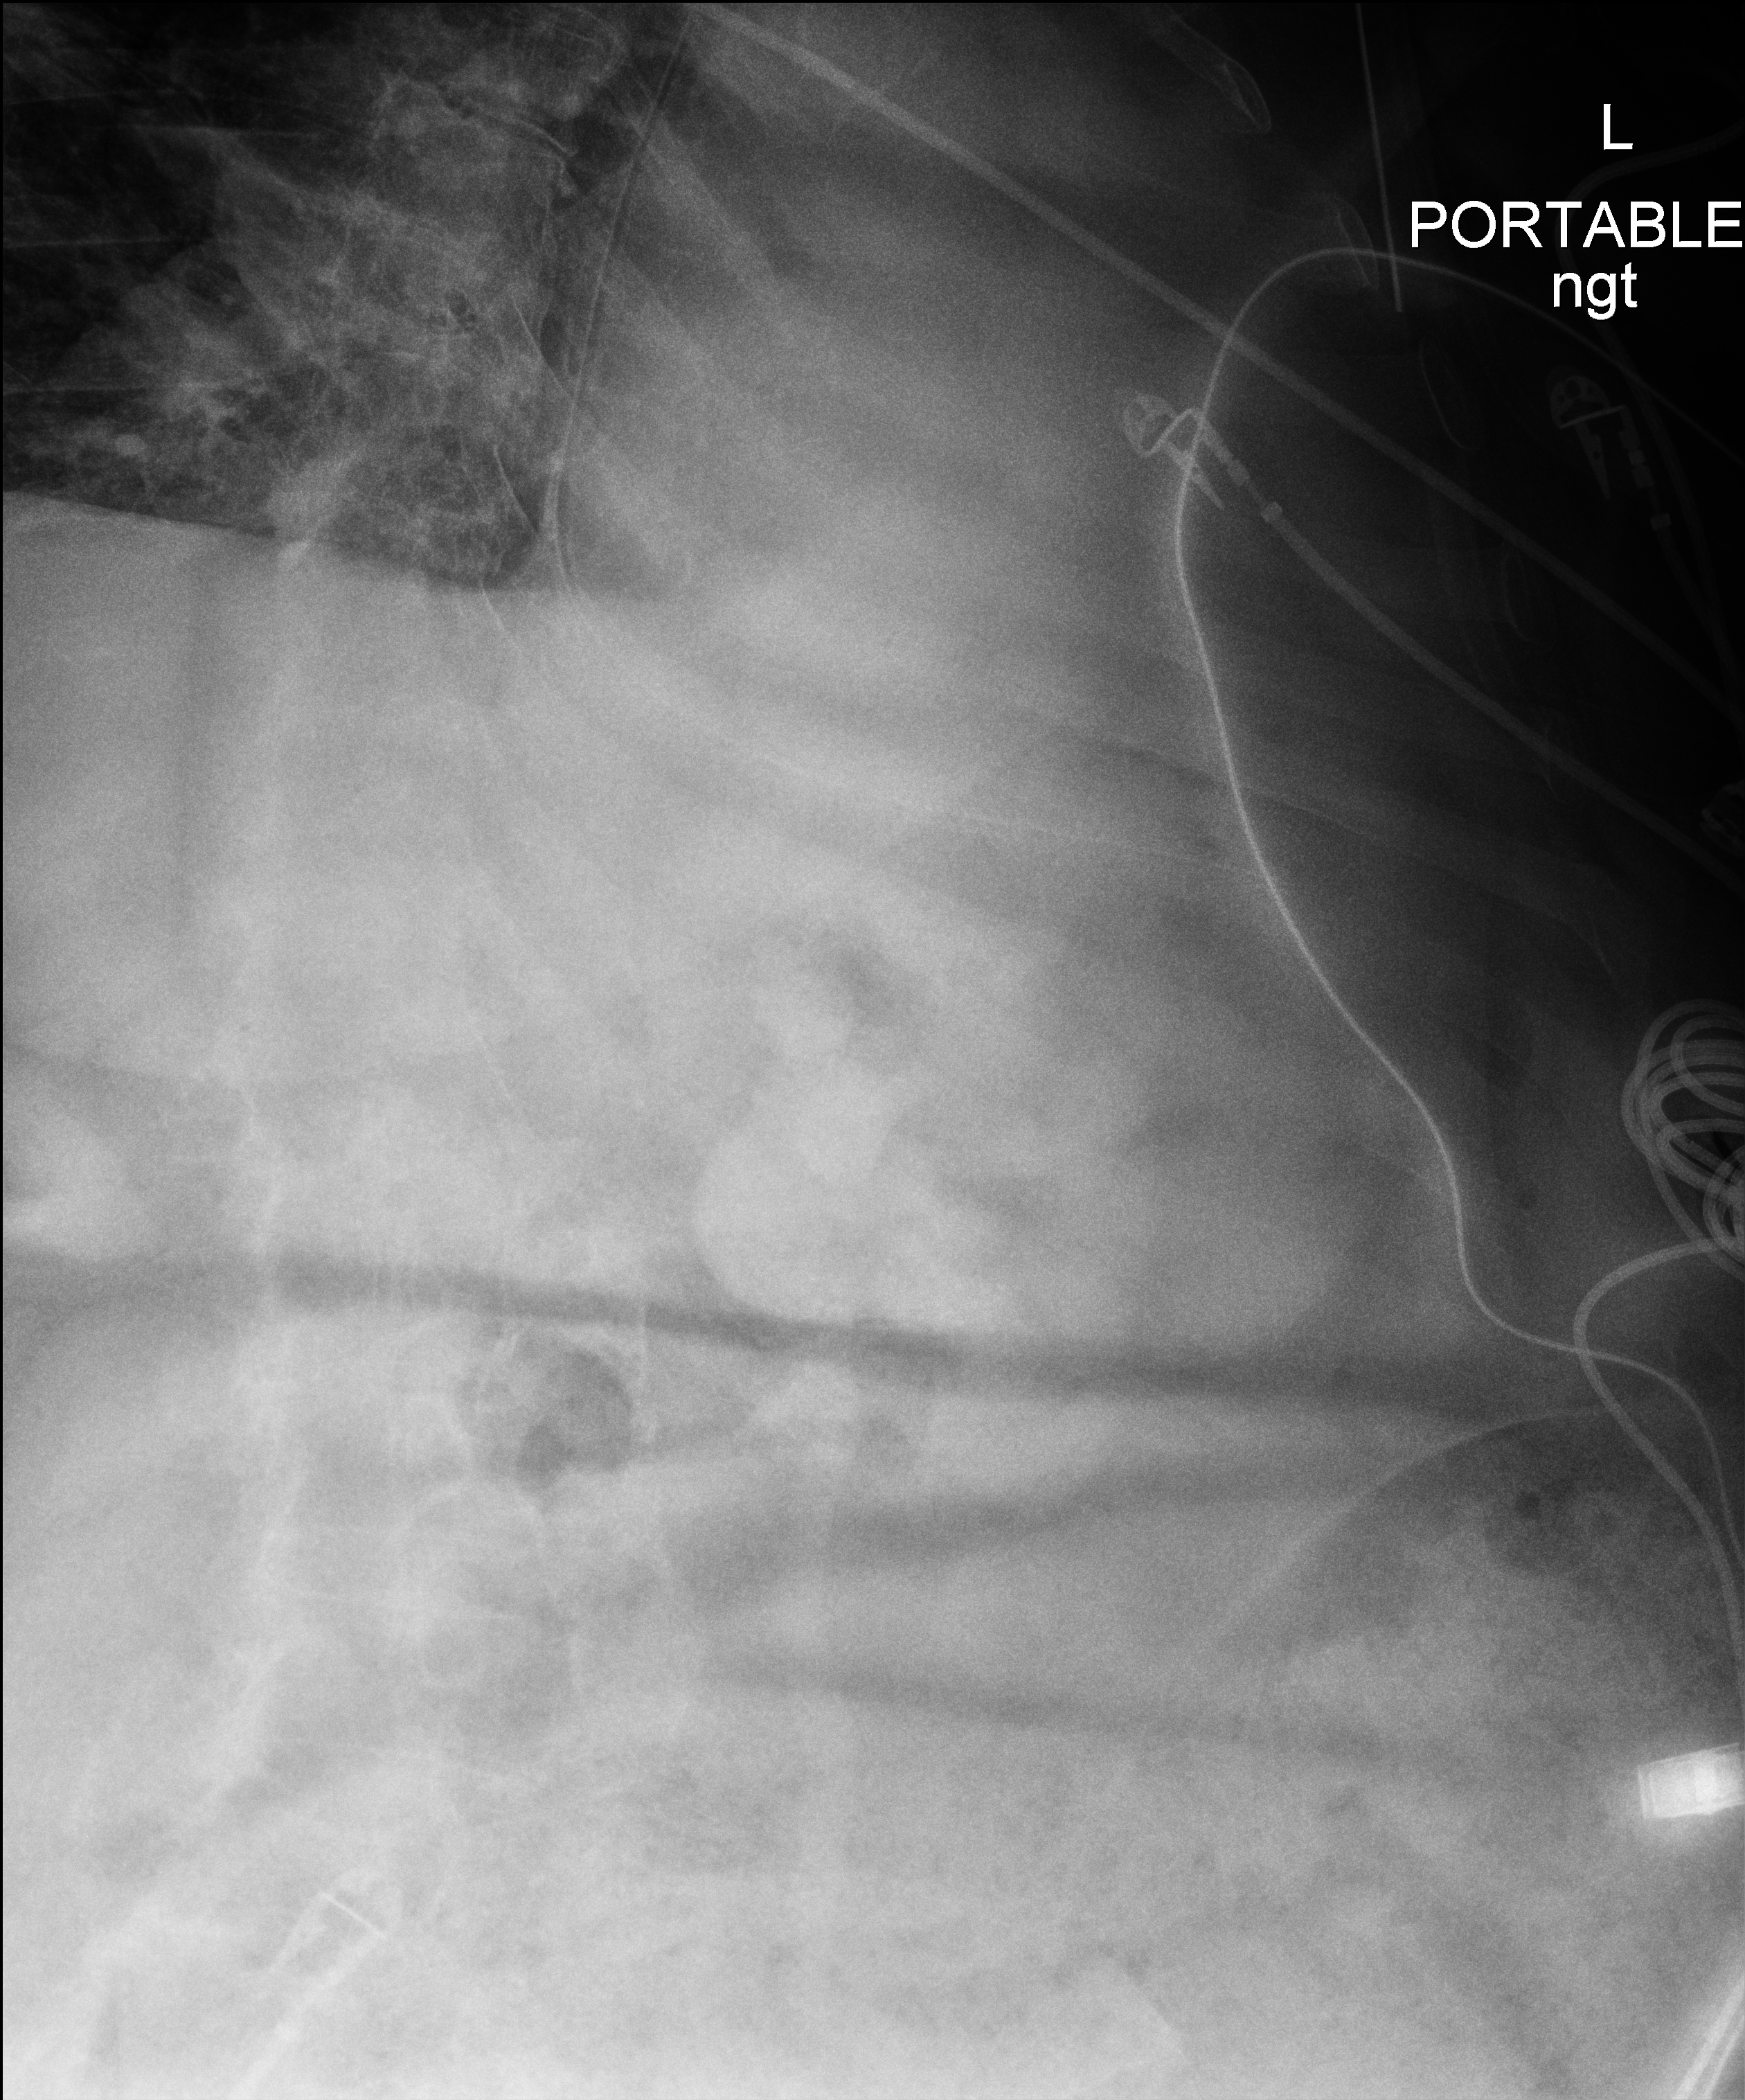
Bedside chest radiograph (digital radiography), anteroposterior (AP) projection. Female patient hospitalised with COVID-19, age 75–90 years.
Admission-level facts for this patient (not findings on this image; timing relative to this image not recorded): length of hospital stay: 5 days; admitted to intensive care during this hospital stay: yes; mechanically ventilated during this hospital stay: no.